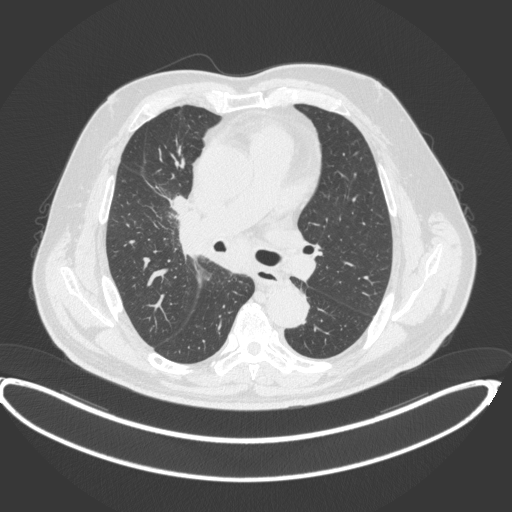
Chest CT, one axial slice; slice 243 of 395 in the series (ordered by position); reconstruction kernel B31f; lung window (W 1500 / L -600 HU); 1 mm slice thickness; 512 × 512 image matrix. Patient: male, 62 years. Case-level facts recorded for this patient, not image findings: clinical TNM (as recorded): T1c N3 M1c.
Annotated regions visible in this slice (bounding box drawn by a radiologist):
- lung tumour (recorded histology: adenocarcinoma): bounding box (x1, y1, x2, y2) in pixels: (164, 188, 194, 216)